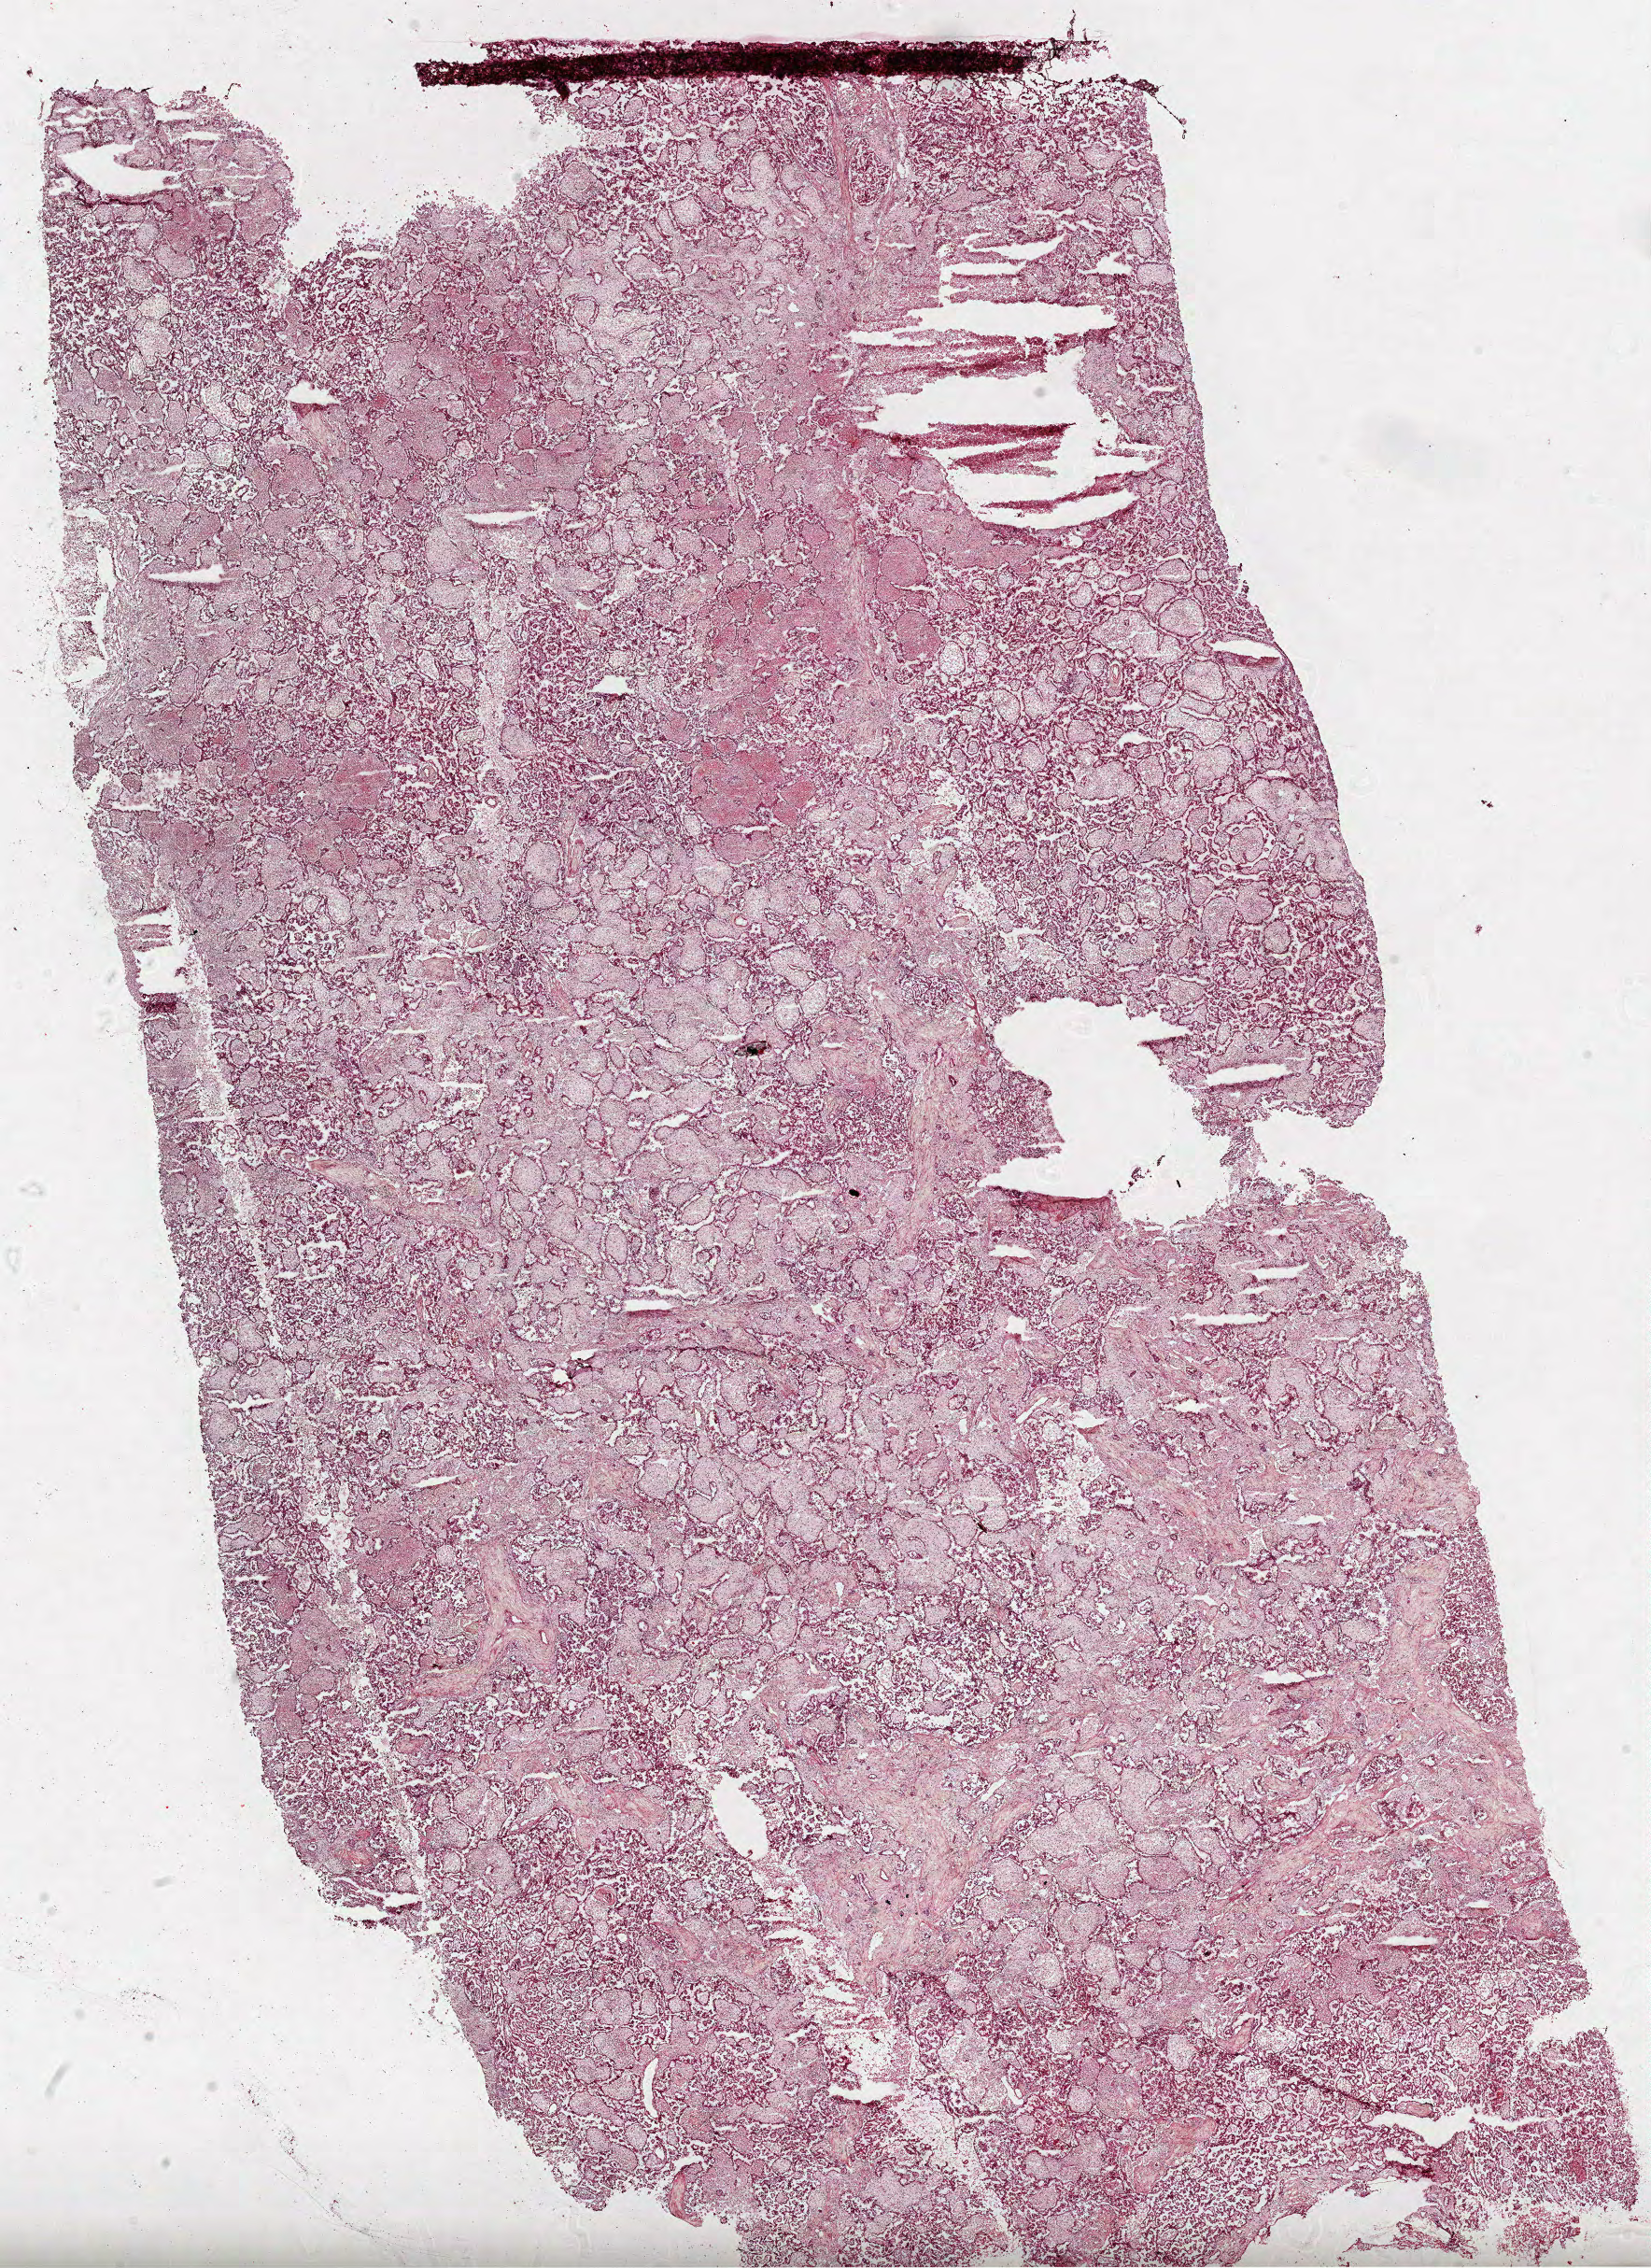
Whole-slide histology image, Hematoxylin and eosin (H&E) stained, whole scanned area (about 14.3 x 19.6 mm) shown as a low-resolution overview; frozen section from the top of the tissue portion; sample: primary tumour, kidney. Male patient; age at initial diagnosis 64 years. Pathologist review of this section (percent, as recorded): tumour cells 100%, tumour nuclei 65%, normal cells 0%, stromal cells 0%, necrosis 0%. Inflammatory infiltration, as recorded: lymphocyte infiltration 0%, monocyte infiltration 20%, neutrophil infiltration 0%.
Histologic diagnosis: Papillary adenocarcinoma, NOS. AJCC pathologic stage: I (7th edition).